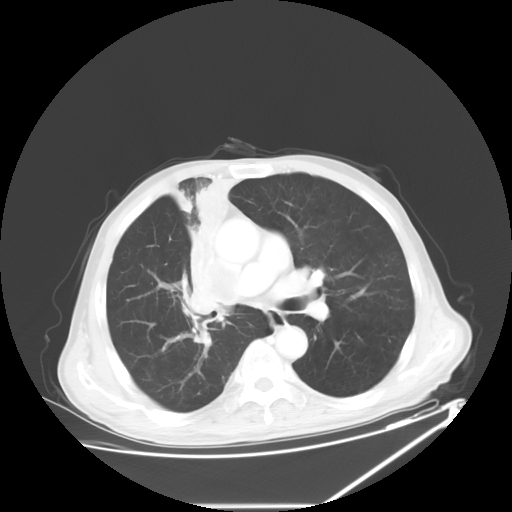
Chest CT, one axial slice. Position 36 of 60 along the scan axis. Reconstruction kernel STANDARD. Lung window (W 1500 / L -600 HU). 512 × 512 image matrix, field of view 410 × 410 mm. Patient: male, 73 years. From the clinical record (not read from this slice): clinical TNM (as recorded): T2a N1 M0.
Annotated regions visible in this slice (rectangle marked by the reading radiologist):
- lung tumour (recorded histology: squamous cell carcinoma): bounding box (x1, y1, x2, y2) in pixels: (171, 175, 243, 325)